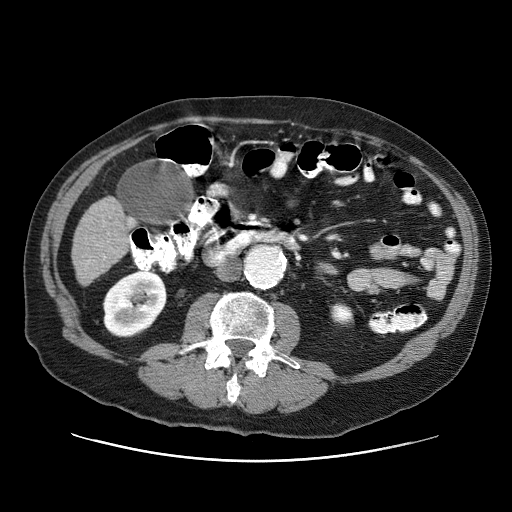
Contrast-enhanced abdominal CT (liver protocol), one axial slice; position 9 of 87 along the scan axis; reconstruction kernel STANDARD; 120 kVp; one of 3 acquisitions stored at this slice position; soft-tissue window (W 400 / L 40 HU); 2.5 mm slice thickness; 512 × 512 image matrix, field of view 400 × 400 mm. From the clinical record (not read from this slice): diagnosis: hepatocellular carcinoma (patient treated with transarterial chemoembolisation; whether this scan precedes or follows treatment is not stated here); TNM stage (as recorded): Stage-IIIA; Child-Pugh class: A; tumour nodularity: multinodular.
Annotated regions visible in this slice (semi-automatically segmented with operator editing):
- liver parenchyma outside the tumour (the mass and vessels are separate outlines, so this box may not span the whole liver): bounding box <72,196,128,284> (left, top, right, bottom; pixels)